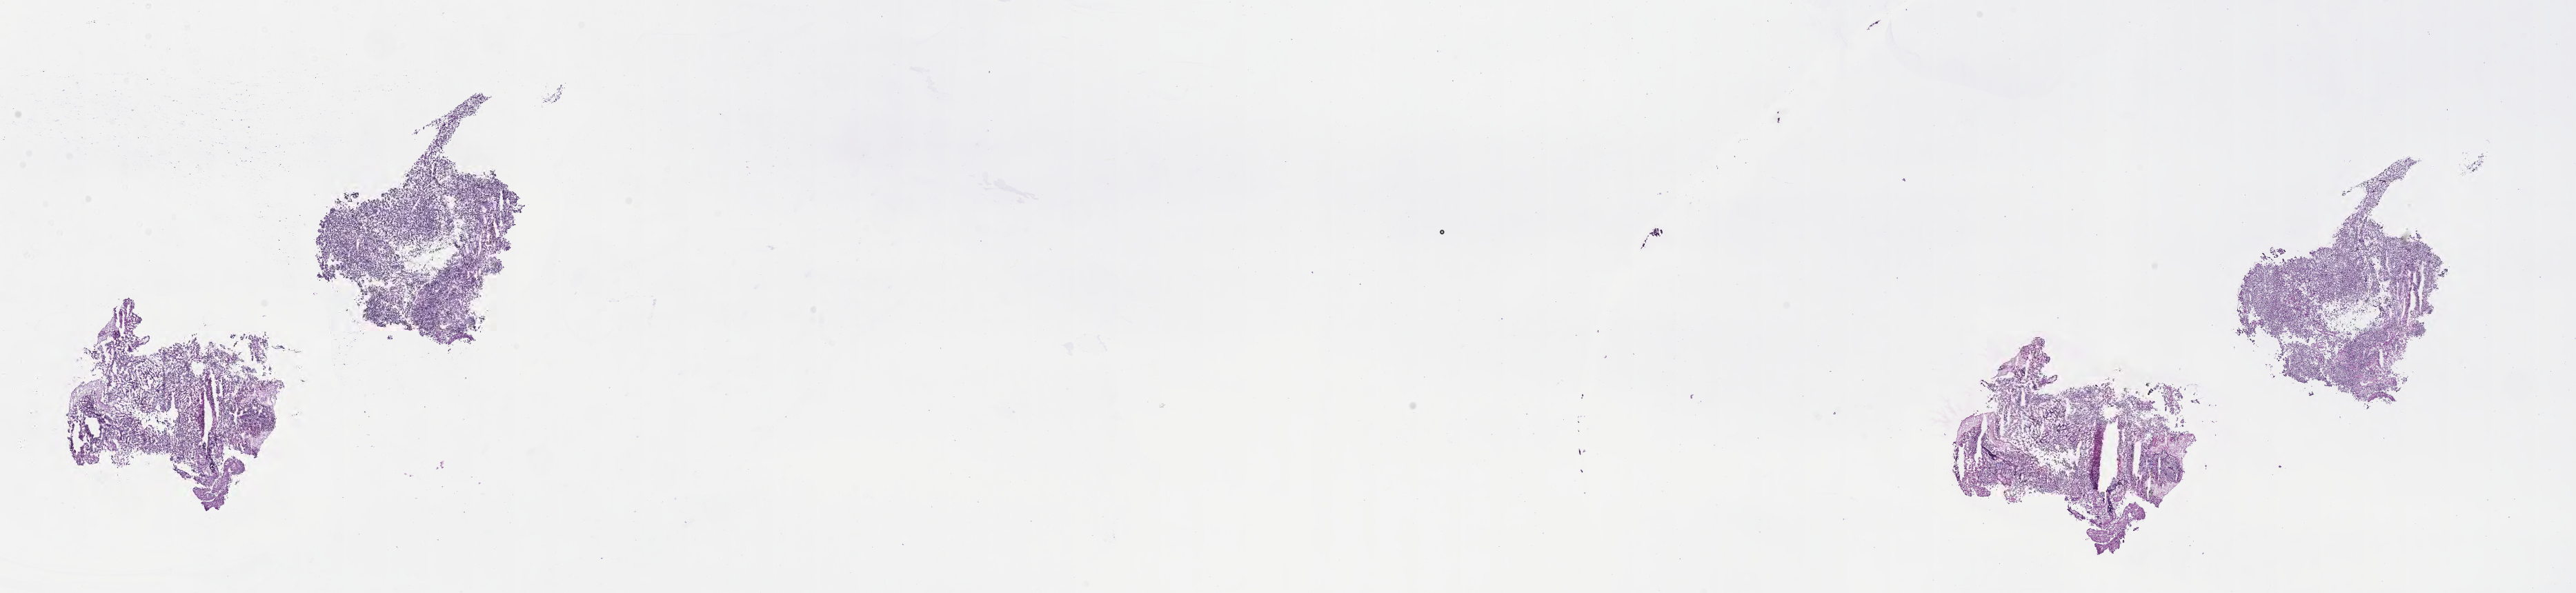
Whole-slide image, hematoxylin and eosin (H&E) stain of tumor tissue from the cerebellum, whole scanned area (about 30.2 x 7.0 mm) shown as a low-resolution overview, frozen section (OCT-embedded). Male patient, age 208 months.
Recorded diagnosis: Medulloblastoma, NOS.